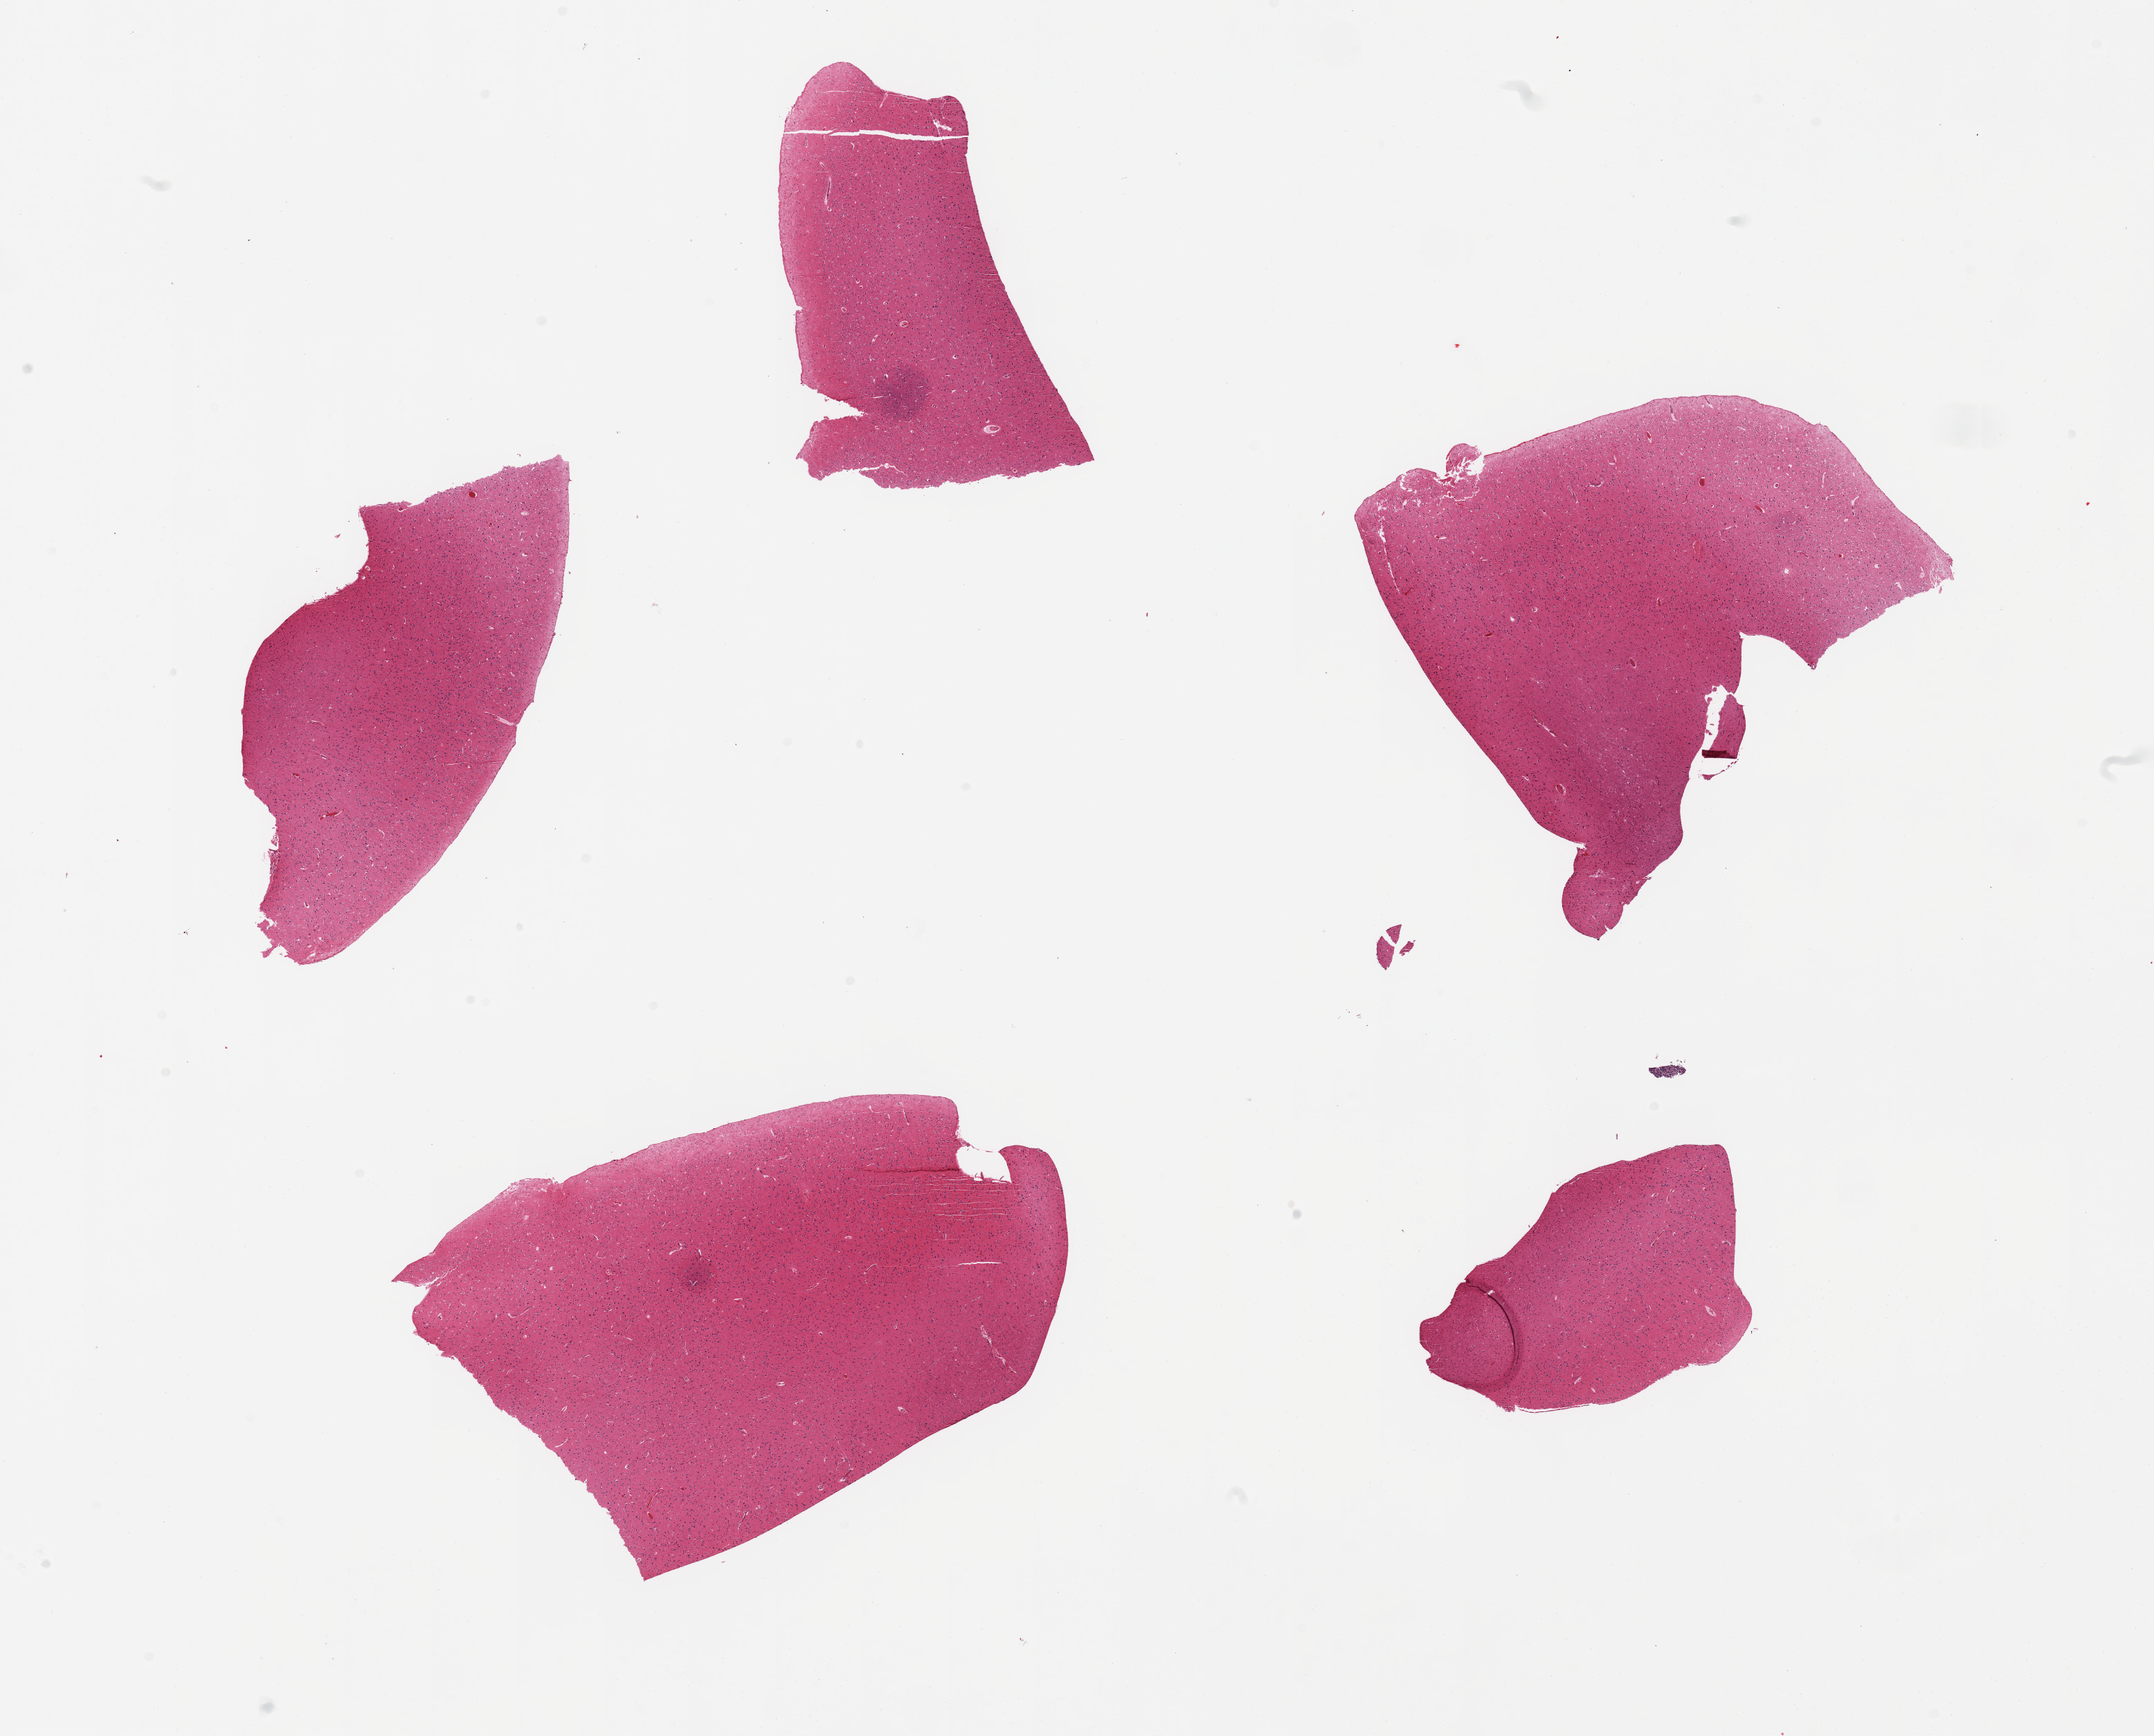
Haematoxylin and eosin whole-slide image — a low-resolution overview of the entire scanned area, about 24.6 x 19.8 mm, PAXgene-fixed, paraffin-embedded tissue, sampled site (target tissue): cerebral cortex, tissue donor sample. Donor sex: male.
Pathologist's review note for this sample: 5 pieces.